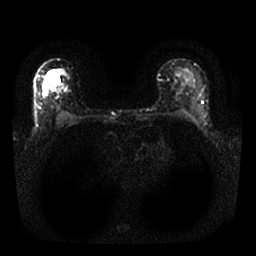
Breast MRI, one axial slice; diffusion-weighted series; image 2 of 4 stored at this slice position (different b-values; order by instance number); 1.5 T; 4 mm slice thickness; 256 × 256 image matrix. Female patient.
Structures marked on this image (manually delineated by an expert):
- tumour on diffusion-weighted imaging: bounding box <47,70,60,87> (left, top, right, bottom; pixels)